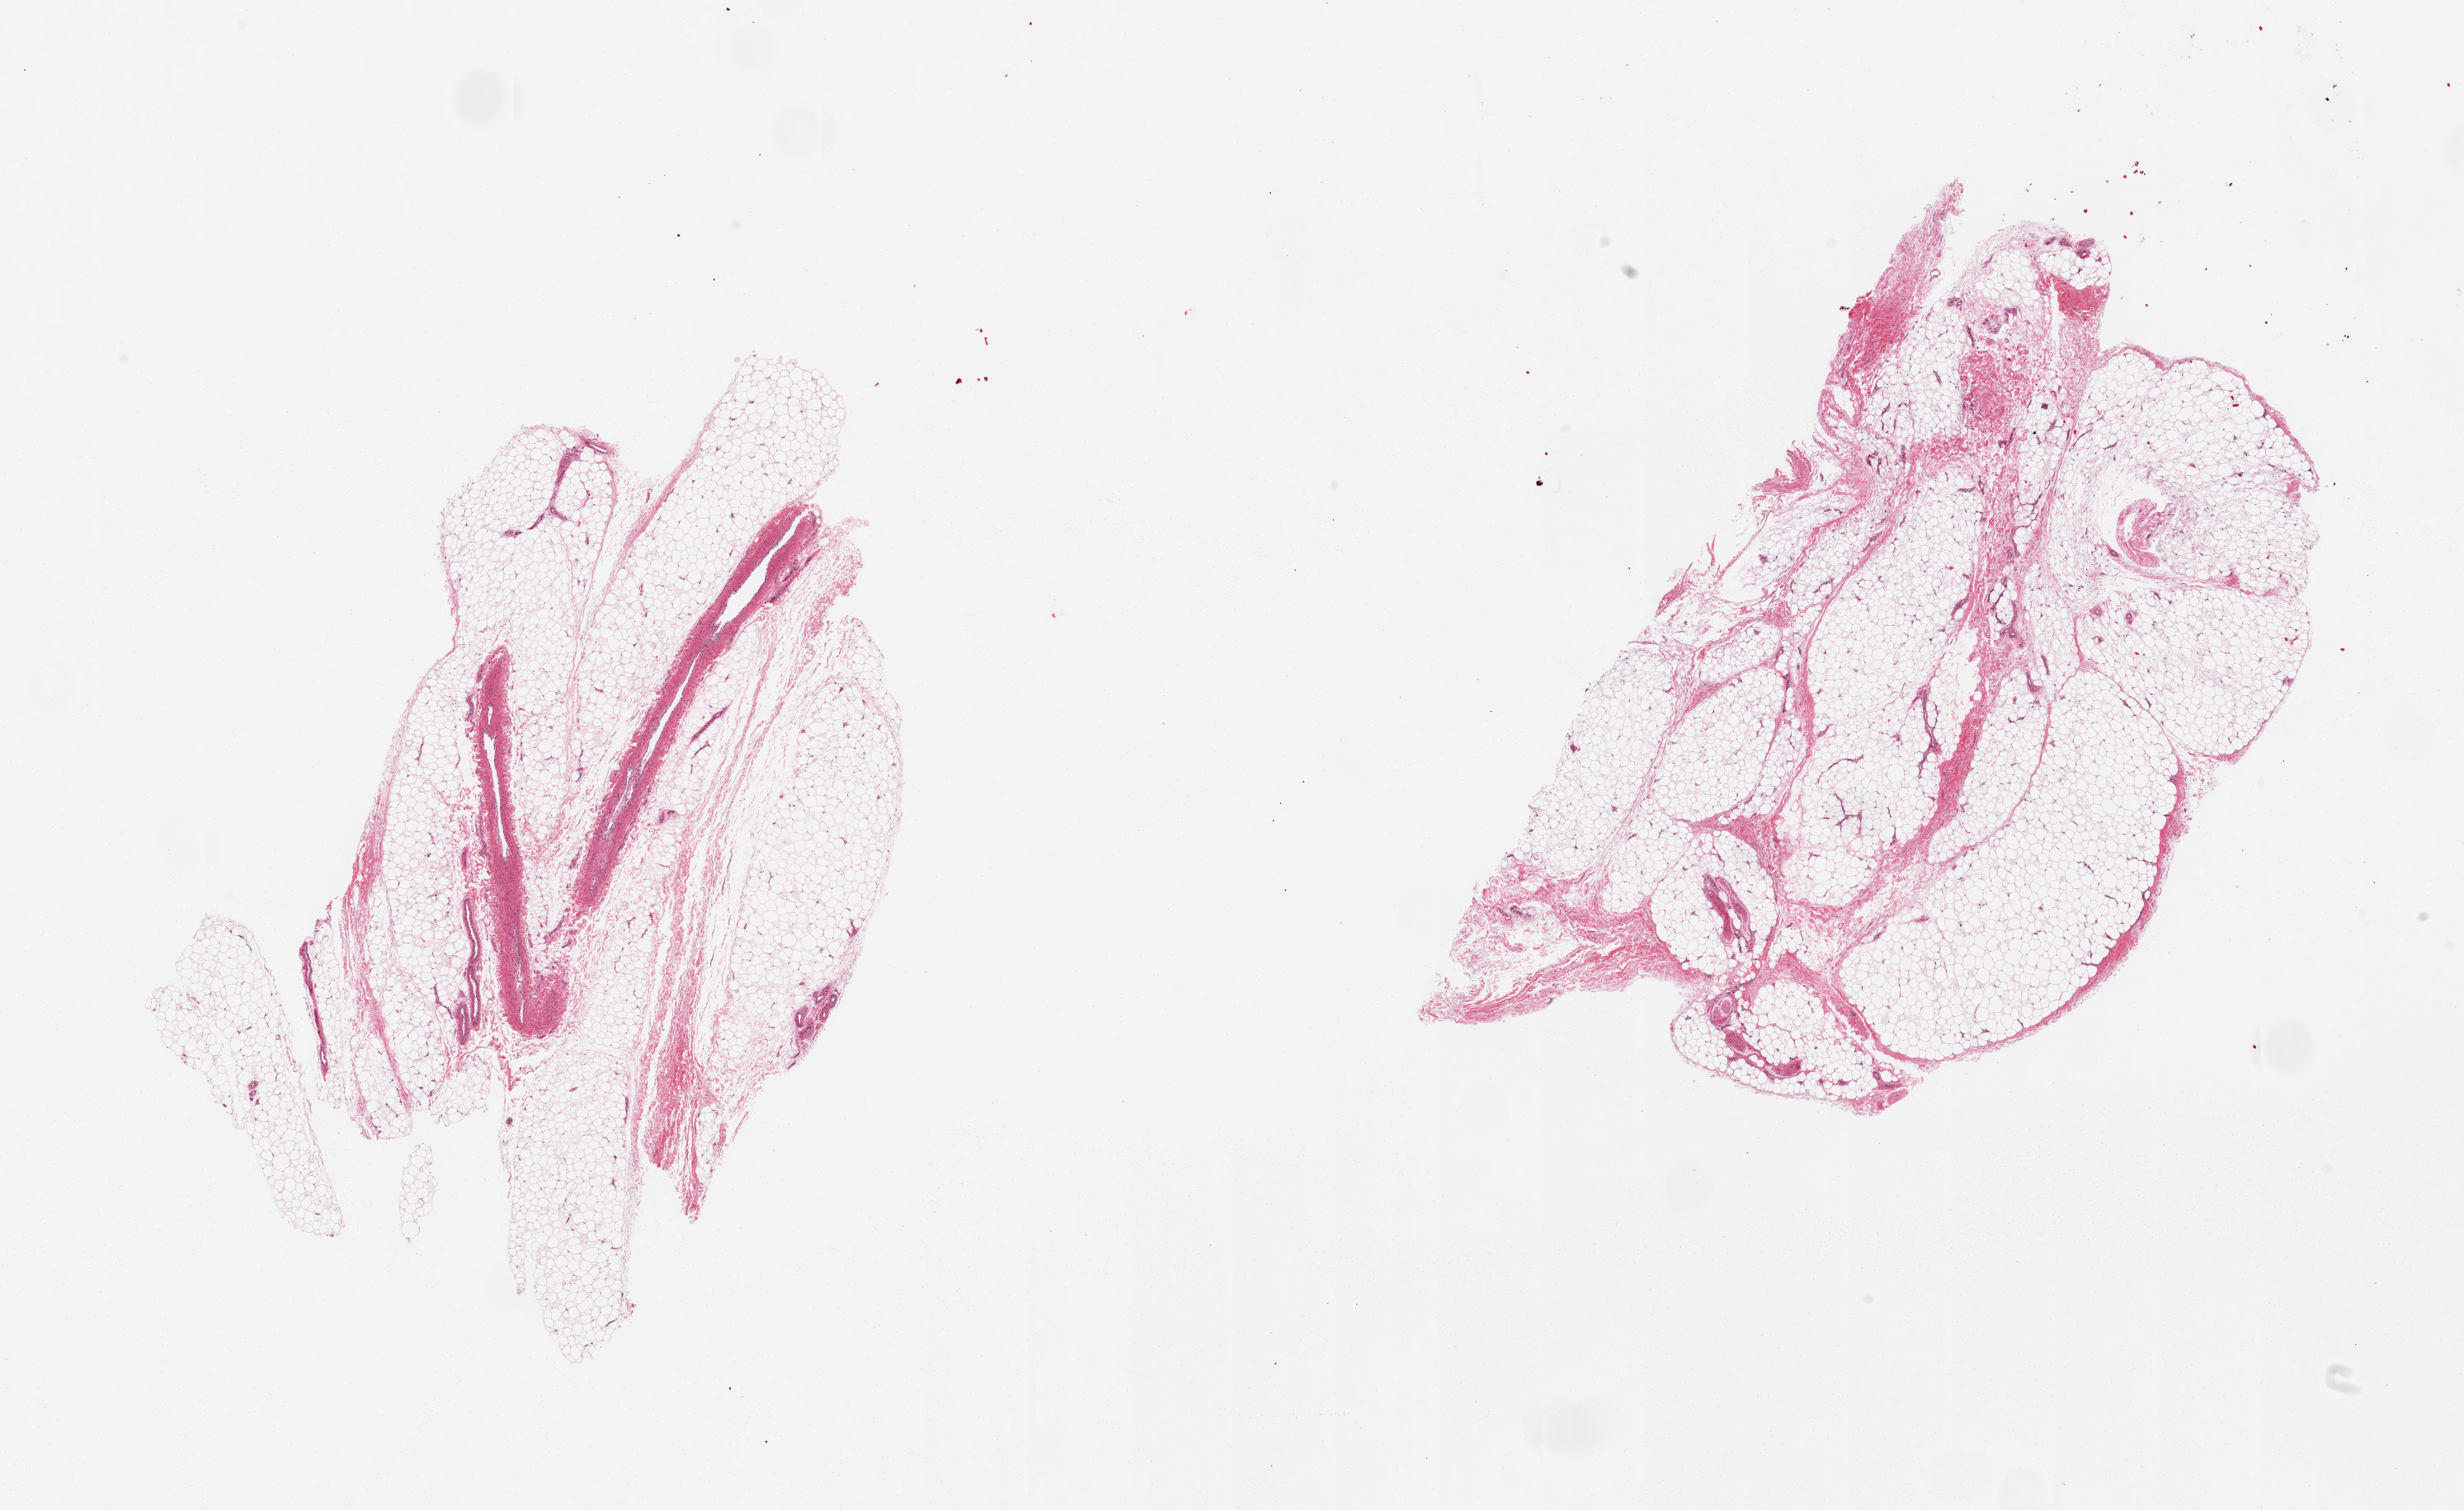
Whole-slide image, H&E stain, brightfield — shown as a low-resolution overview of the whole scanned area (about 23.6 x 14.5 mm, slide scanned at 20x). PAXgene-fixed, paraffin-embedded tissue. Sampled site (target tissue): adipose tissue. Tissue donor sample. Male donor.
Reviewer comment on this tissue sample: 2 pieces; 10% fibrovascular content.